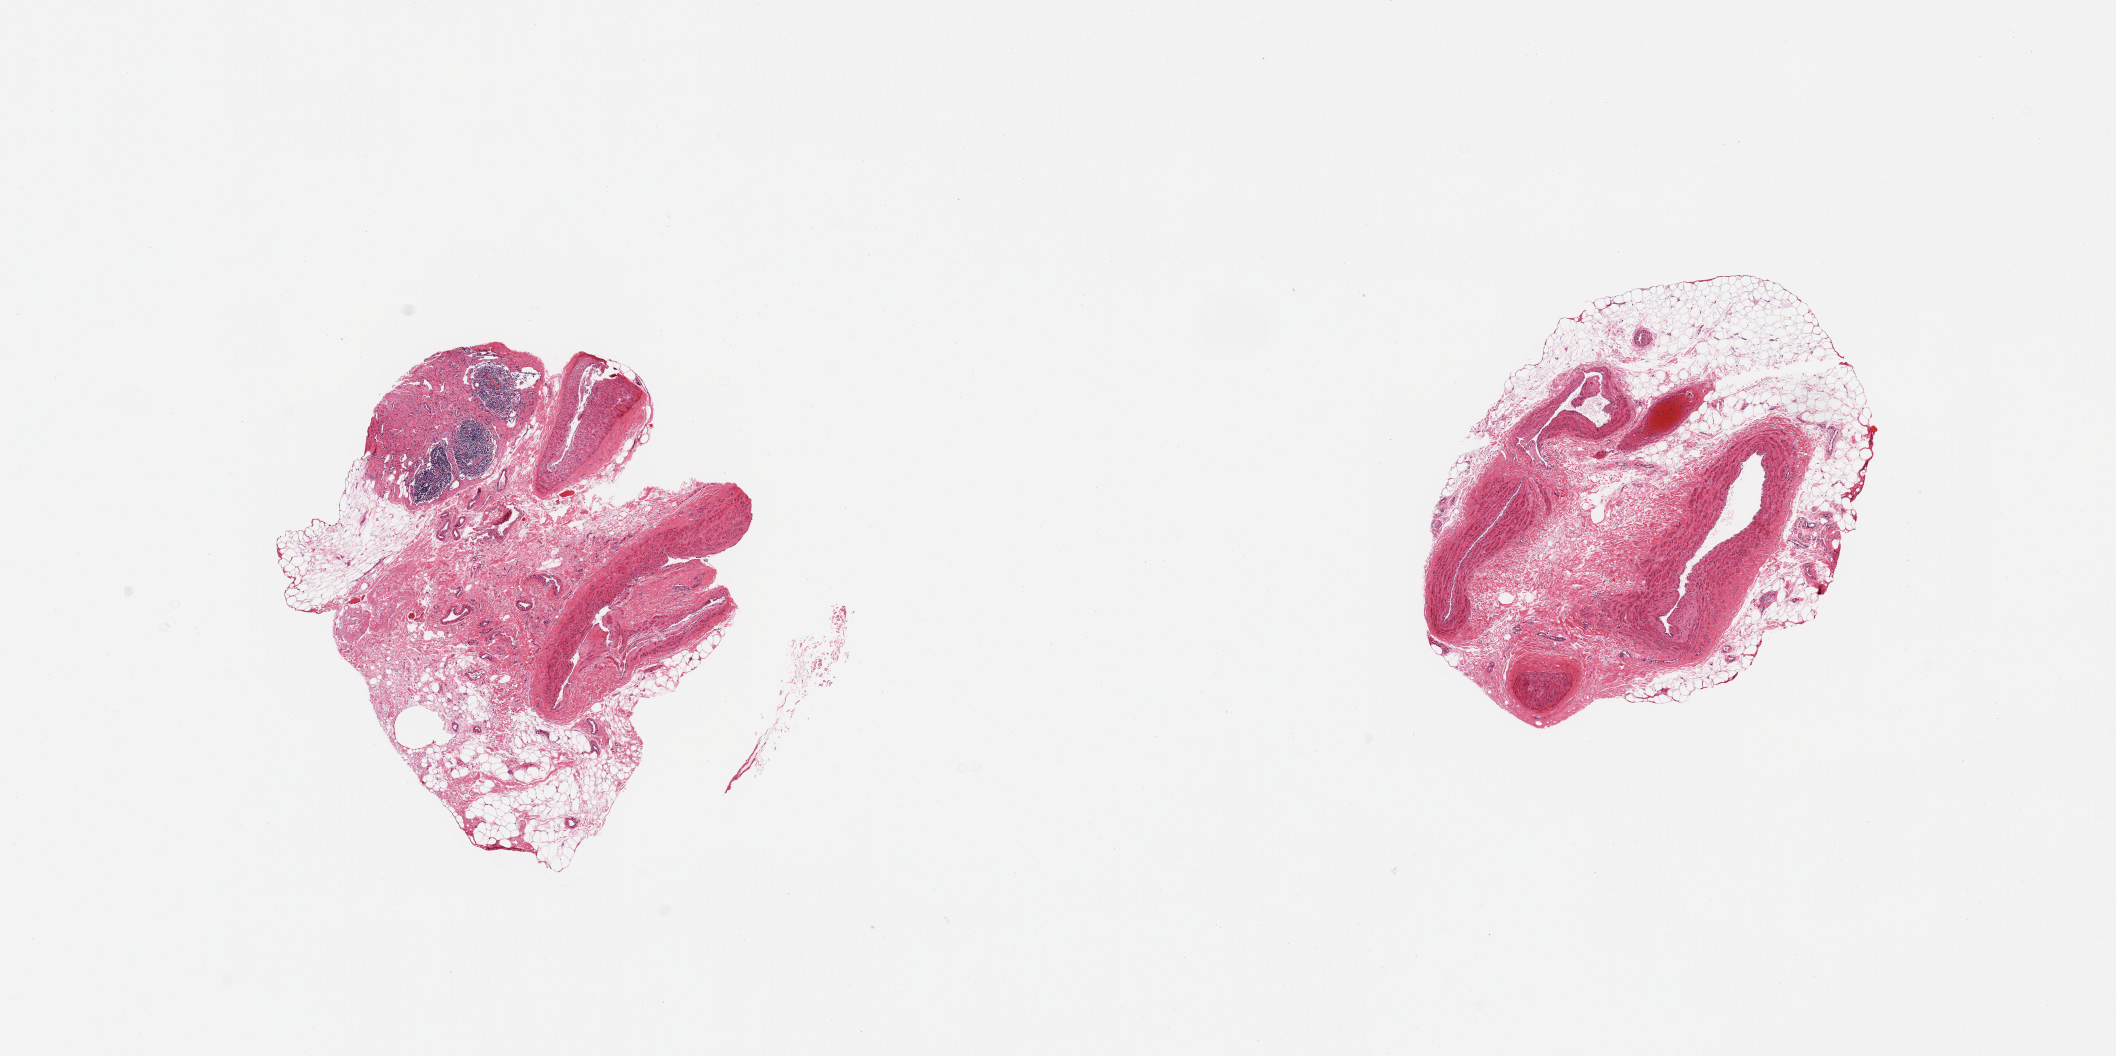
Whole-slide image, hematoxylin and eosin (H&E) stain, low-resolution overview of the scanned area, about 16.7 x 8.4 mm (from a 20x scan), PAXgene-fixed, paraffin-embedded tissue, sampled site (target tissue): tibial nerve, donor tissue sample. Male donor.
* pathologist's review note for this sample: 2 pieces; not nerve; vessels/fat/fibrous and lymphoid tissue